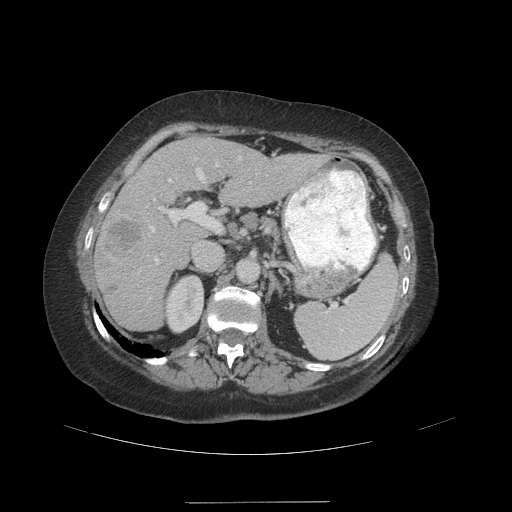
Contrast-enhanced abdominal CT (liver protocol), one axial slice. Position 63 of 99 along the scan axis. 140 kVp. Soft-tissue window (W 400 / L 40 HU). 2.5 mm slice thickness. 512 × 512 image matrix, field of view 440 × 440 mm. Case-level facts recorded for this patient, not image findings: diagnosis: hepatocellular carcinoma (patient treated with transarterial chemoembolisation; whether this scan precedes or follows treatment is not stated here); TNM stage (as recorded): Stage-IVA; Child-Pugh class: A; tumour nodularity: multinodular.
Annotated regions visible in this slice (semi-automatically segmented with operator editing):
- liver parenchyma outside the tumour (the mass and vessels are separate outlines, so this box may not span the whole liver): bounding box [x1, y1, x2, y2] px = [94, 138, 325, 330]
- mass: [104, 220, 140, 297]
- liver vessels: [149, 157, 252, 264]